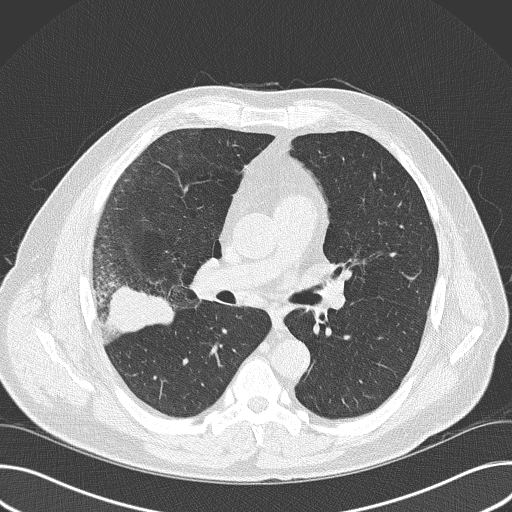
Chest CT (low-dose screening protocol), one axial image. Baseline screening round. Lung window (W 1500 / L -600 HU). 2 mm slice thickness. 120 kVp. 512 × 512 image matrix, field of view 380 × 380 mm. Male participant, aged 56 years at enrolment. Current smoker at enrolment.
• Expert reader's lesion annotation, bounding box [x1, y1, x2, y2] px = [79, 255, 182, 357].
• Screening reader's record for this exam (one nodule recorded; not confirmed to be the boxed lesion): non-calcified nodule or mass ≥4 mm, right upper lobe, 6 × 5 mm, spiculated (stellate) margins, soft tissue attenuation.
• Lung cancer was diagnosed 16 days after this screen: adenocarcinoma, NOS, right upper lobe, poorly differentiated (G3), stage IIB (AJCC 6th edition), 60 mm at pathology.